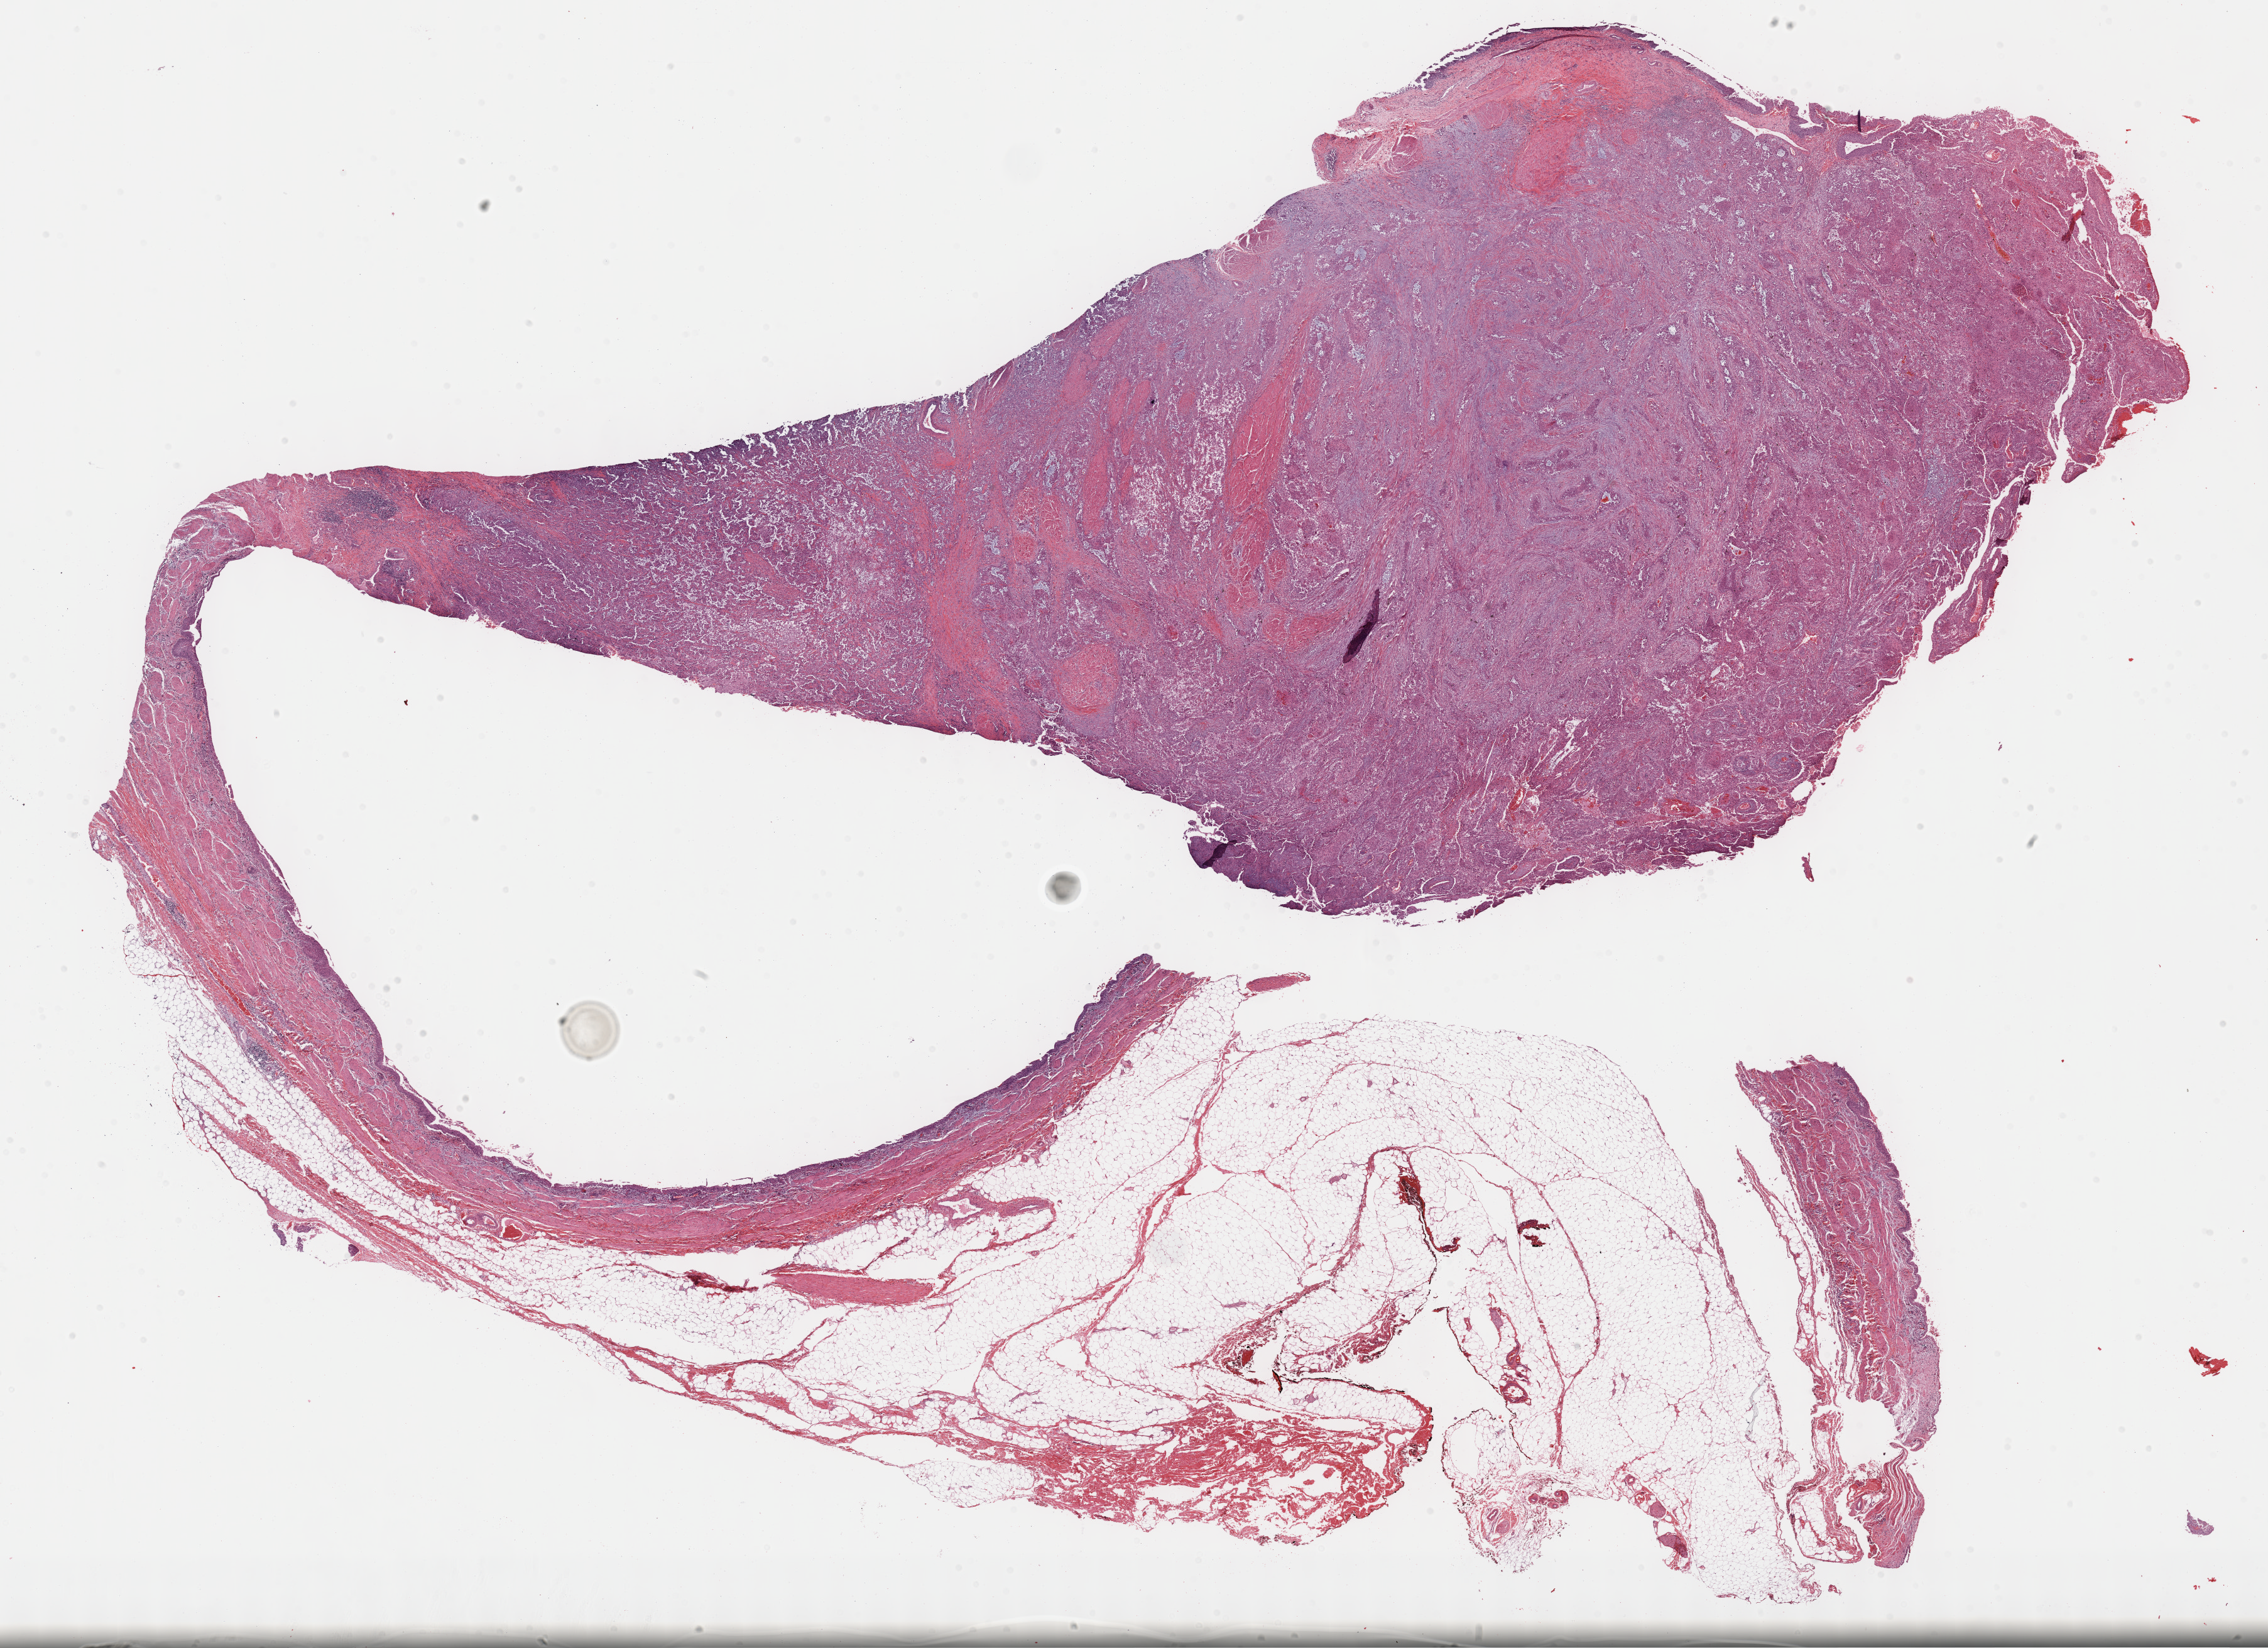
Digitized H&E-stained tissue section (whole slide), shown as a low-resolution overview of the whole scanned area (about 29.2 x 21.2 mm); formalin-fixed paraffin-embedded (FFPE) diagnostic section; bladder, primary tumour sample. Male patient; age at initial diagnosis 48 years. Histologic grade: high grade.
AJCC pathologic stage: IV (6th edition). Pathologic diagnosis: Transitional cell carcinoma.